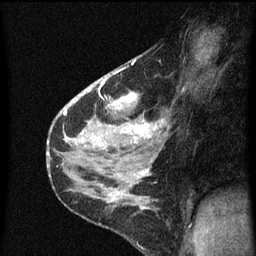
Breast MRI (dynamic contrast-enhanced), one sagittal slice. Position 41 of 60 along the scan axis. Dynamic contrast-enhanced series, image 2 of 3 at this slice position (ordered by acquisition). 1.5 T. TE 4.2 ms, TR 8 ms. 256 × 256 image matrix, field of view 180 × 180 mm. Patient: female, 38 years.
Annotated regions visible in this slice (semi-automatically segmented with operator editing):
- analysis volume of interest (the breast-tissue region the enhancement analysis was run in; not a lesion): box from (x=80, y=56) to (x=167, y=151) px
- tumour enhancement mask (voxels above the 70 % enhancement threshold inside the analysis volume of interest): (x=82, y=72)–(x=157, y=147)